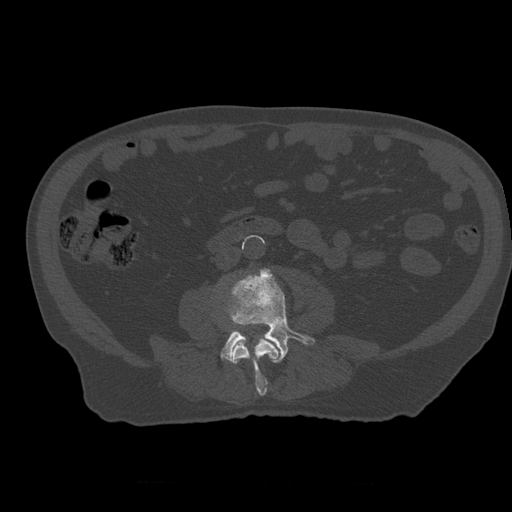
CT including the spine, one axial slice. Position 175 of 399 along the scan axis. 120 kVp. Bone window (W 1800 / L 400 HU). 512 × 512 image matrix. Patient age 73 years. Case-level facts recorded for this patient, not image findings: primary cancer: prostate.
Annotated regions visible in this slice (semi-automatically segmented with operator editing):
- L3 vertebra: bounding box <231,336,283,396> (left, top, right, bottom; pixels)
- L4 vertebra: <221,268,315,363>